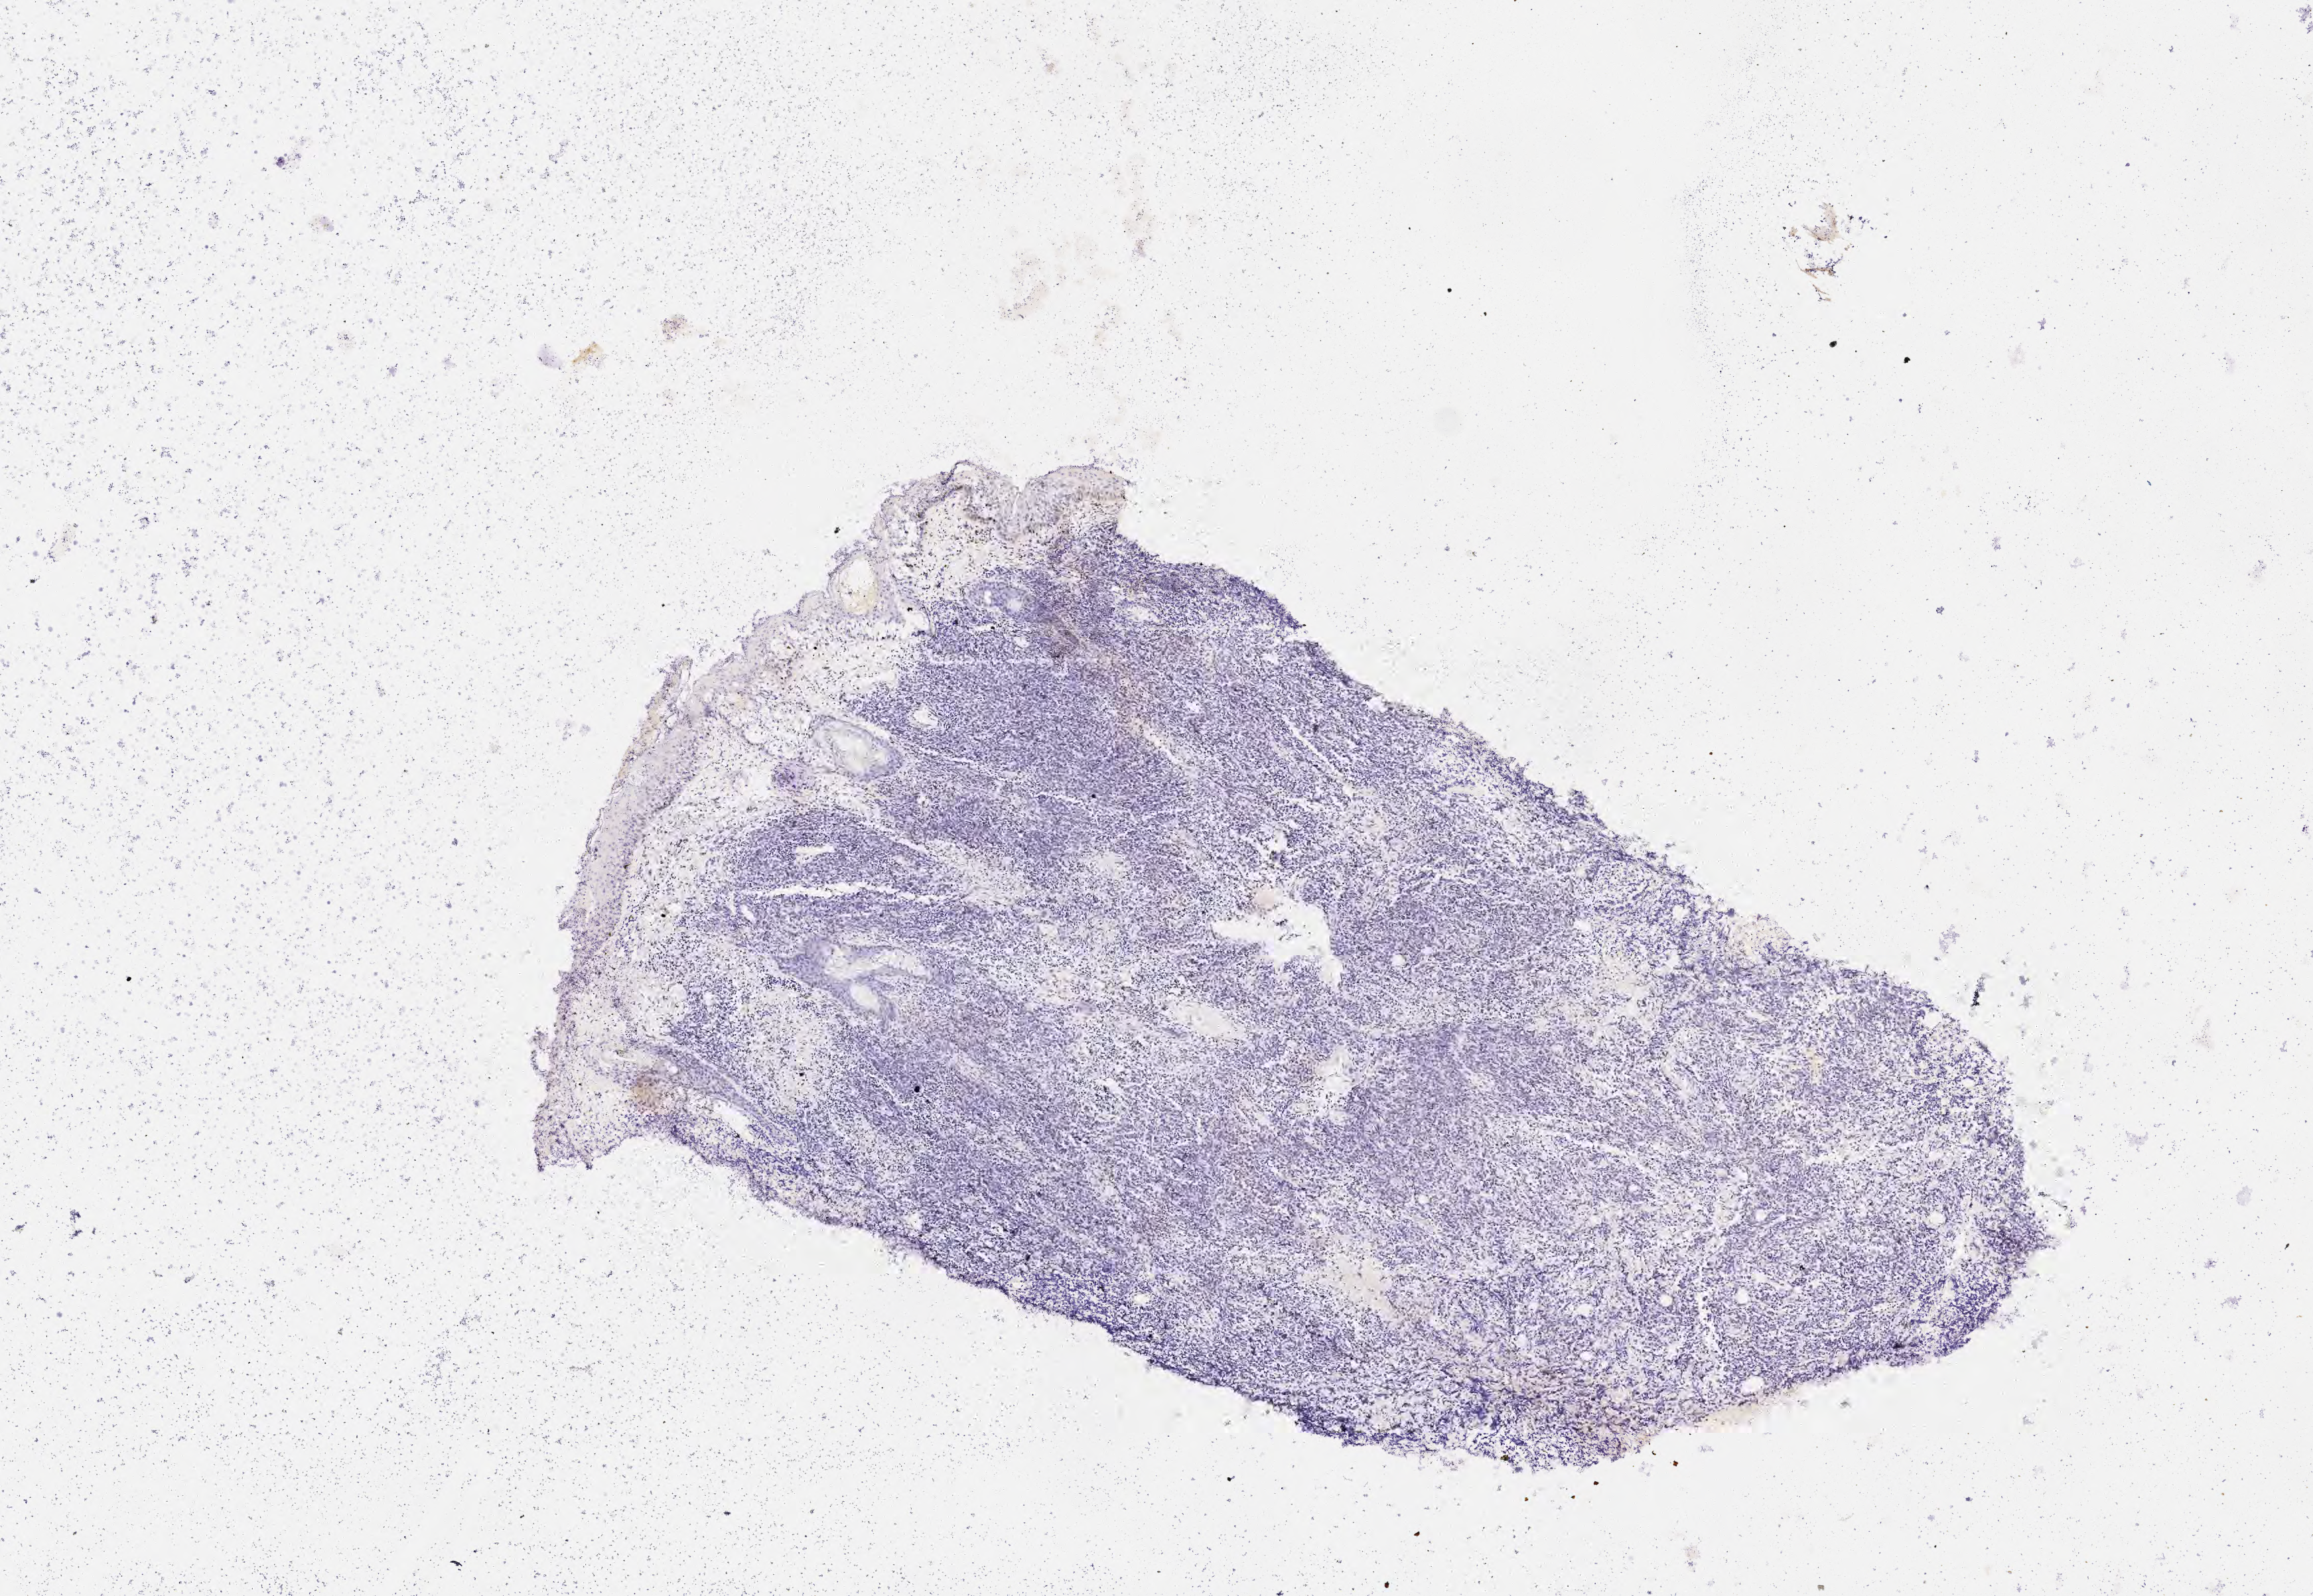
In-situ hybridisation whole-slide image, Epstein–Barr virus-encoded RNA (EBER) probe, whole scanned area (about 7.0 x 4.9 mm) shown as a low-resolution overview. Tumor tissue. Male patient, age 41 years.
Histologic diagnosis: Diffuse large B-cell lymphoma, NOS.